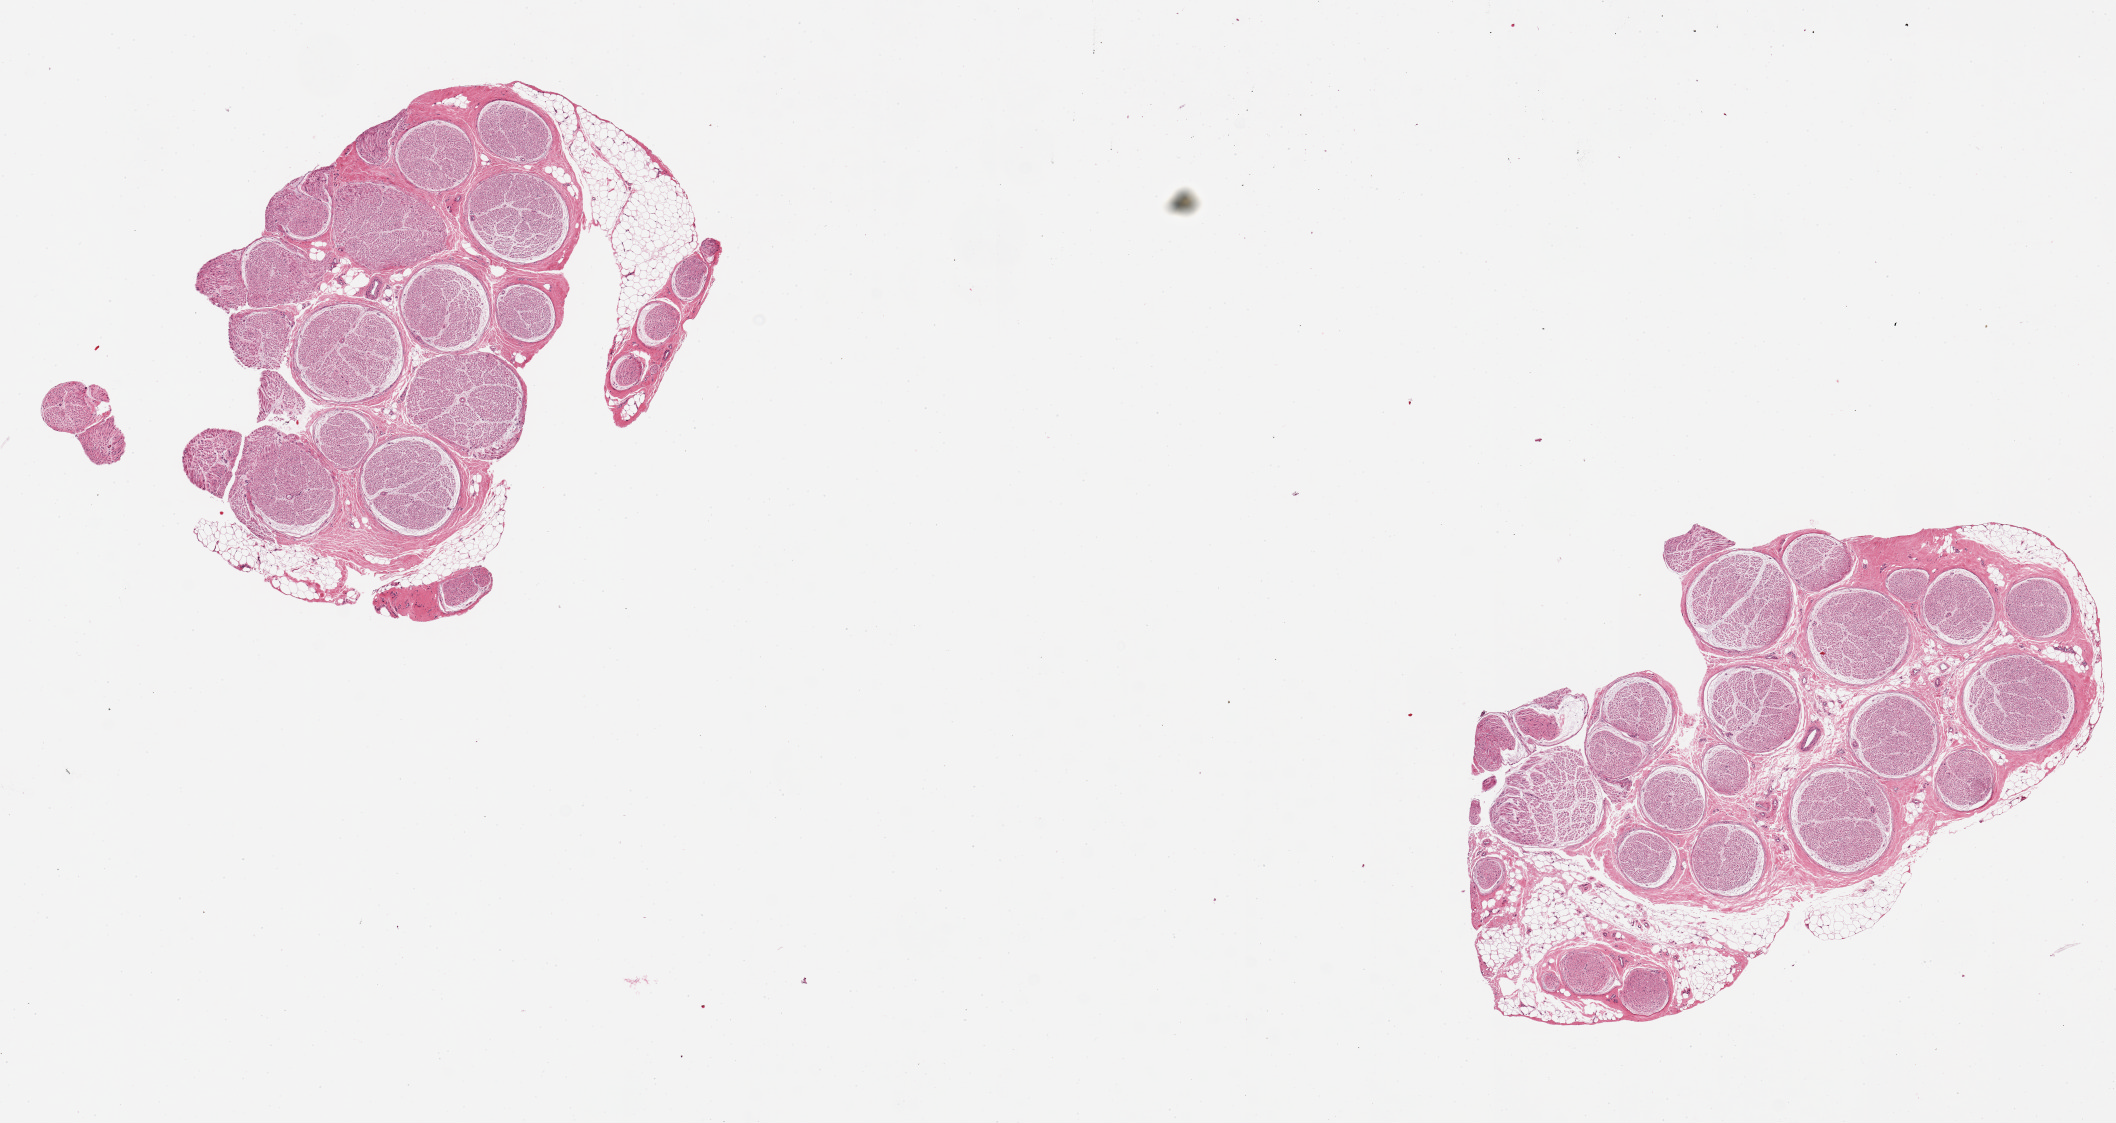
Whole-slide image, haematoxylin and eosin stain, brightfield, shown as a low-resolution overview of the whole scanned area (about 16.7 x 8.9 mm); PAXgene-fixed paraffin-embedded (PFPE) section; sampled site (target tissue): tibial nerve; tissue donor sample. Donor sex: female.
Pathologist's review note for this sample: 2 pieces. 5x4 & 6x4mm; 10% adherent adipose.